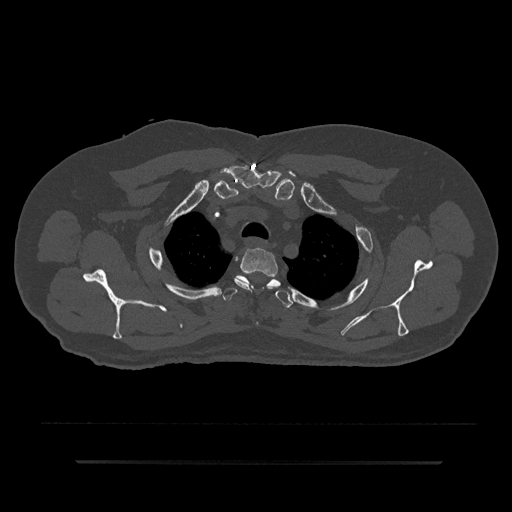
CT including the spine, one axial slice; position 682 of 797 along the scan axis; reconstruction kernel Br40s/3; bone window (W 1800 / L 400 HU); 0.5 mm slice thickness; 512 × 512 image matrix. Patient: male, 59 years. Case-level facts recorded for this patient, not image findings: primary cancer: bile ducts; vertebrae with lytic lesions (as recorded): T10.
Annotated regions visible in this slice (semi-automatically segmented with operator editing):
- T2 vertebra: bounding box (x1, y1, x2, y2) in pixels: (234, 248, 278, 291)
- T3 vertebra: (223, 275, 293, 308)